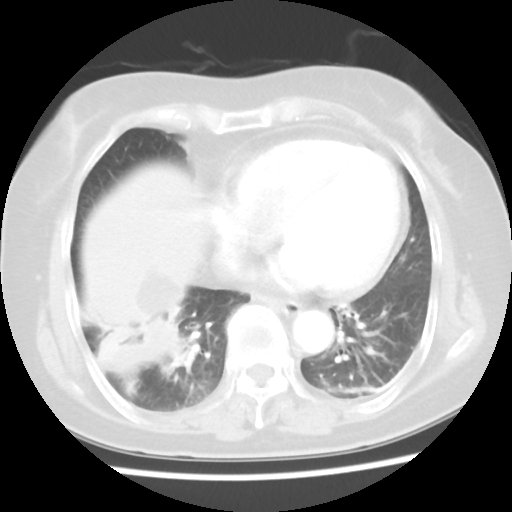
Chest CT, one axial slice; slice 15 of 45 in the series (ordered by position); reconstruction kernel STANDARD; lung window (W 1500 / L -600 HU); 5 mm slice thickness; 512 × 512 image matrix, field of view 312 × 312 mm. Female patient, age 65 years. Case-level facts recorded for this patient, not image findings: clinical TNM (as recorded): T2 N3 M0.
Outlined on this slice (rectangle marked by the reading radiologist):
- lung tumour (recorded histology: adenocarcinoma): bounding box (x1, y1, x2, y2) in pixels: (126, 307, 195, 383)